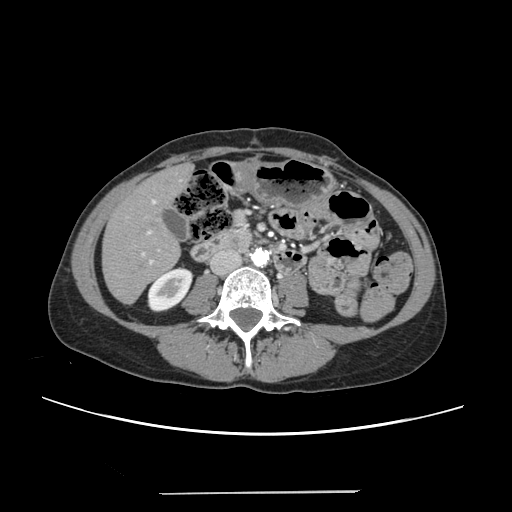
Contrast-enhanced abdominal CT, one axial slice. 120 kVp. Soft-tissue window (W 400 / L 40 HU). 1.25 mm slice thickness. 512 × 512 image matrix, field of view 371 × 371 mm. Female patient, age 60 years. Case-level facts recorded for this patient, not image findings: diagnosis: colorectal cancer liver metastases, imaged before liver resection; multiple liver metastases: no; largest metastasis: 1.5 cm; disease in both lobes: no.
Outlined on this slice (outlined manually by an expert reader):
- liver: bounding box (x1, y1, x2, y2) in pixels: (104, 166, 190, 302)
- planned liver remnant (the part of the liver to remain after resection): (104, 172, 179, 302)
- portal vein (with intrahepatic branches): (141, 200, 156, 264)